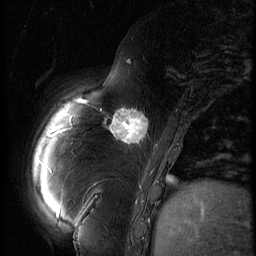
Breast MRI (dynamic contrast-enhanced), one sagittal slice. Position 14 of 60 along the scan axis. 3 images stored at this slice position (order not interpretable as contrast timing). 1.5 T. TE 4.2 ms, TR 9 ms. 256 × 256 image matrix. Patient: female, 57 years. From the clinical record (not read from this slice): setting: breast cancer imaged before/during neoadjuvant chemotherapy; receptor status: triple-negative.
Structures marked on this image (semi-automatically segmented with operator editing):
- analysis volume of interest (the breast-tissue region the enhancement analysis was run in; not a lesion): box from (x=106, y=101) to (x=157, y=152) px
- tumour enhancement mask (voxels above the 140 % enhancement threshold inside the analysis volume of interest): (x=110, y=110)–(x=149, y=145)